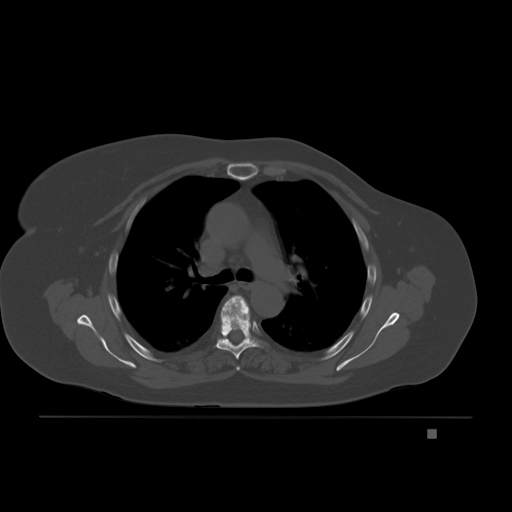
CT including the spine, one axial slice; position 145 of 221 along the scan axis; bone window (W 1800 / L 400 HU); 512 × 512 image matrix, field of view 474 × 474 mm. Patient: female, 63 years. Case-level facts recorded for this patient, not image findings: primary cancer: breast.
Outlined on this slice (semi-automatic segmentation, software-assisted and operator-edited):
- T4 vertebra: box from (x=237, y=367) to (x=240, y=370) px
- T5 vertebra: (x=215, y=295)–(x=262, y=360)
- T6 vertebra: (x=229, y=337)–(x=246, y=342)